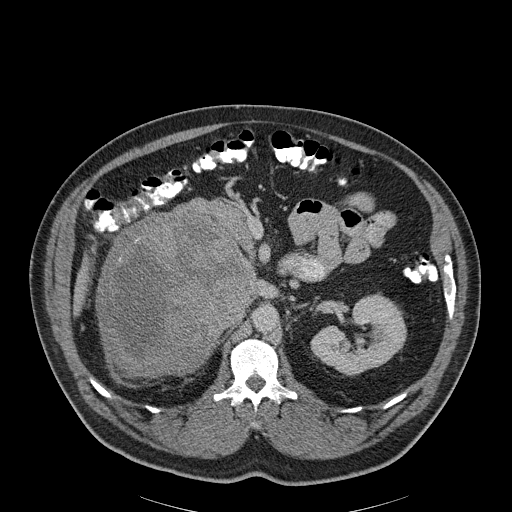
Contrast-enhanced abdominal CT, one axial slice. Slice 122 of 186 in the series (ordered by position). Reconstruction kernel B30f. 120 kVp. Soft-tissue window (W 400 / L 40 HU). 512 × 512 image matrix, field of view 464 × 464 mm. Male patient, age 56 years. From the clinical record (not read from this slice): diagnosis: adrenocortical carcinoma; tumour side: right adrenal; tumour size at pathology: 18 cm; Ki-67 index: 2 %; stage (as recorded): 3.
Outlined on this slice (semi-automatic segmentation, software-assisted and operator-edited):
- mass: bounding box <98,215,245,376> (left, top, right, bottom; pixels)